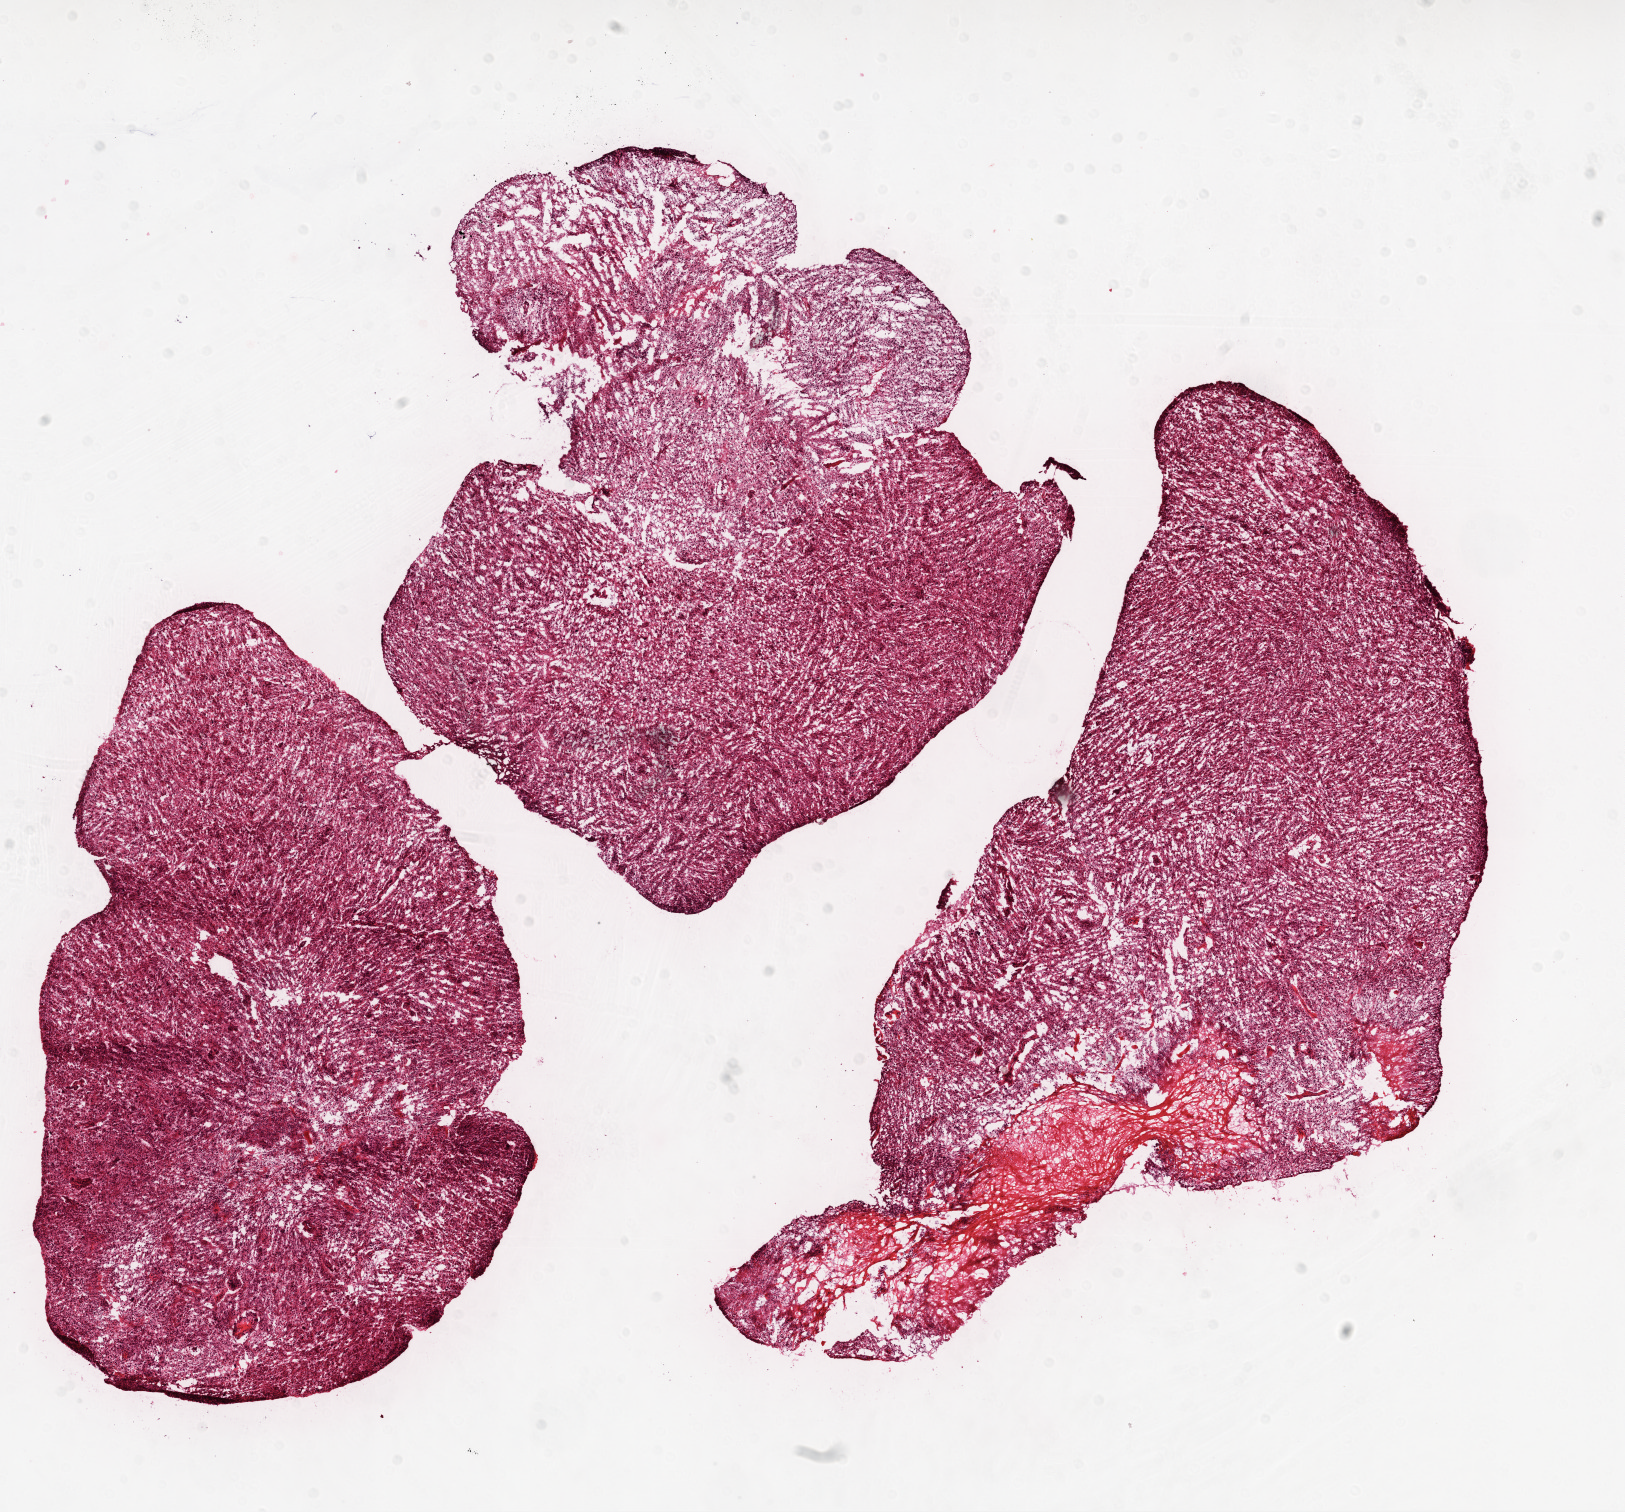
H&E whole-slide image, low-resolution overview of the scanned area, about 13.0 x 12.1 mm (slide scanned at 20x). Frozen section from the top of the tissue portion. Brain, primary tumour sample. Patient: female, age at initial diagnosis 58 years. Composition of this section per pathologist review: tumour cells 90%, tumour nuclei 95%, normal cells 0%, stromal cells 2%, necrosis 8%.
Diagnosis: Glioblastoma.